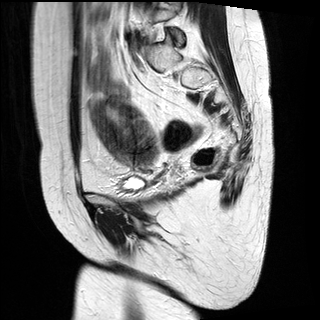
Pelvic MRI for cervical cancer, one sagittal slice; T2-weighted; 1.5 T; TE 89 ms, TR 2740 ms; 320 × 320 image matrix. Female patient, age 49 years.
Structures marked on this image (outlined manually by an expert reader):
- uterus and cervix: bounding box (x1, y1, x2, y2) in pixels: (89, 91, 159, 166)